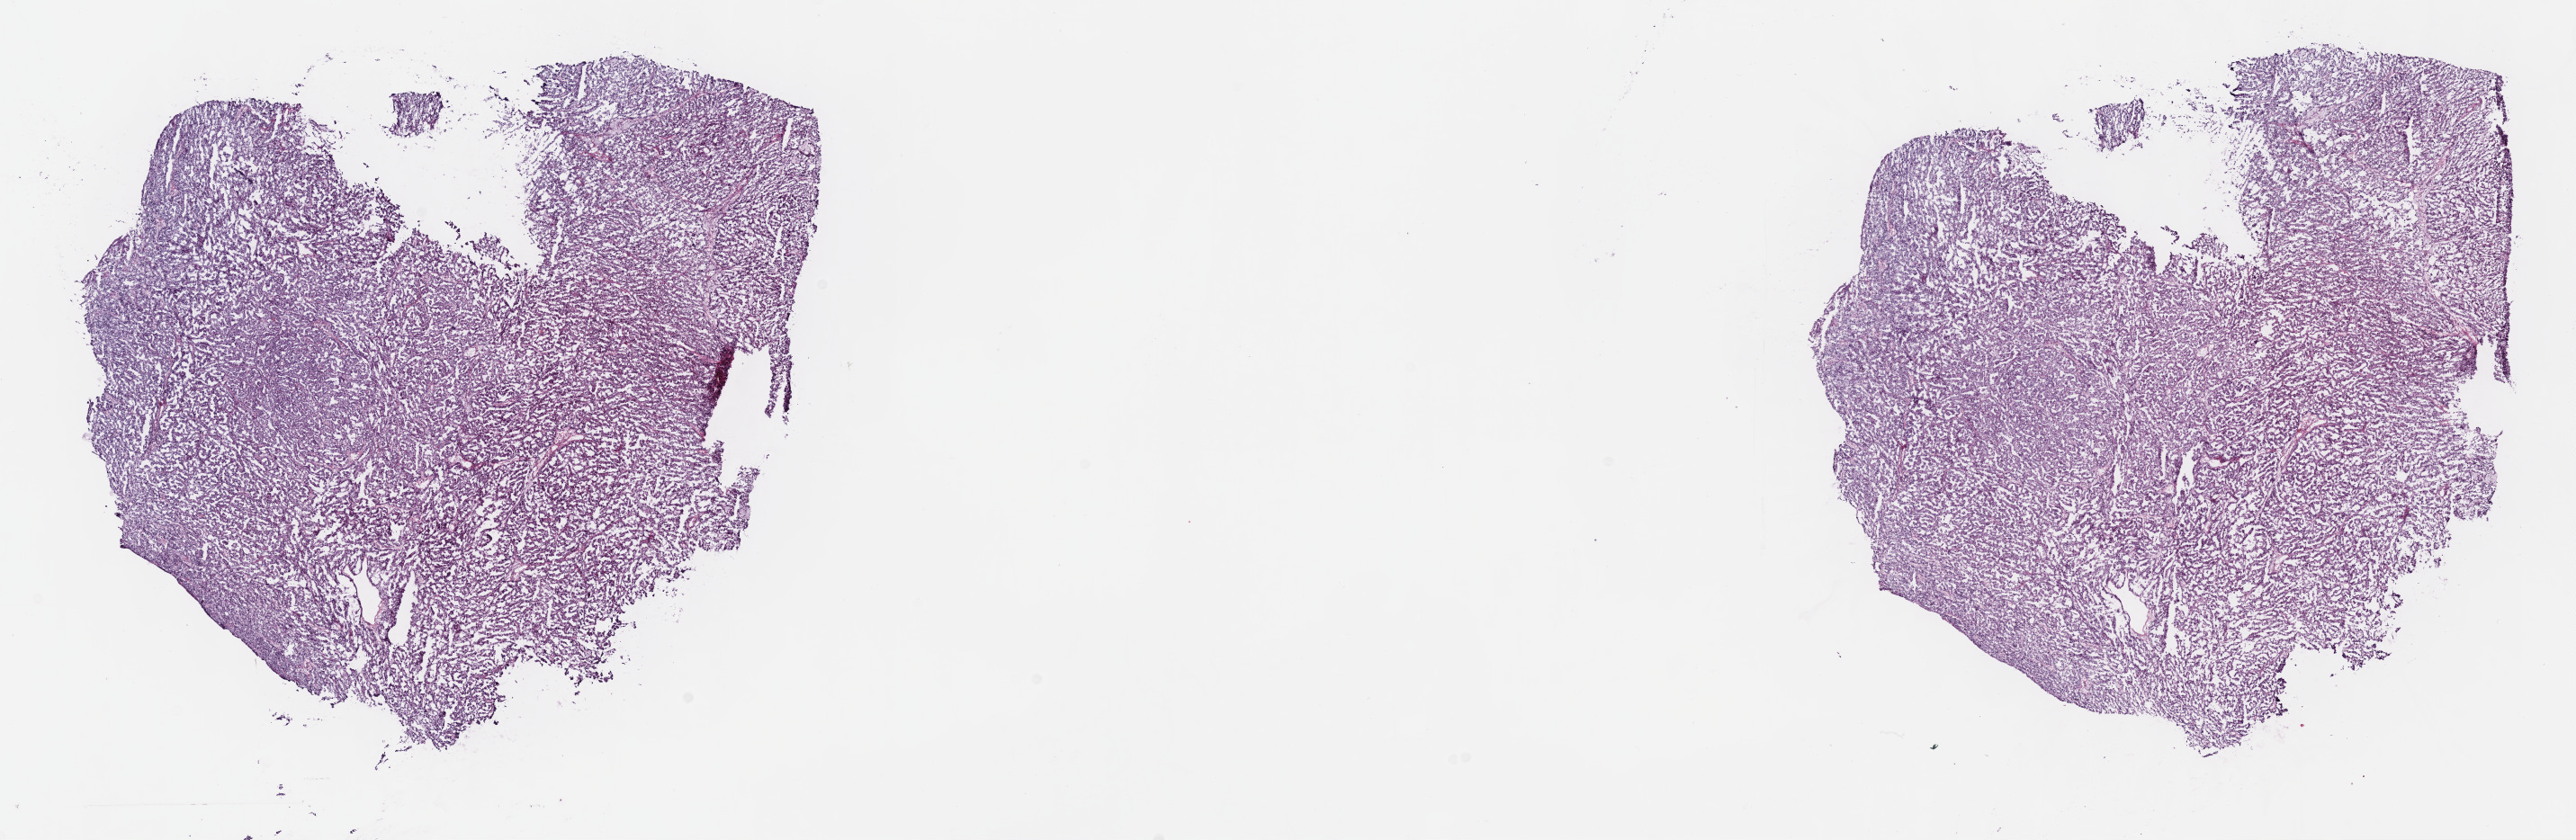
Hematoxylin and eosin (H&E) stained whole-slide image, shown as a low-resolution overview of the whole scanned area (about 23.2 x 7.6 mm); frozen section from the top of the tissue portion; kidney, primary tumour sample. Patient: male, age at initial diagnosis 74 years.
Diagnosis: Papillary adenocarcinoma, NOS.